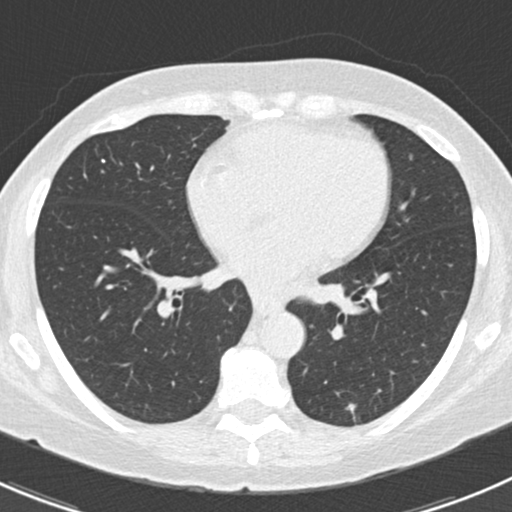
Chest CT (low-dose screening protocol), one axial image. Second screening round (one year after baseline). Lung window (W 1500 / L -600 HU). Slice 86 of 166 in the series. 512 × 512 image matrix. Female, age 64 years at enrolment.
Expert-annotated lung lesion, bounding box [x1, y1, x2, y2] px = [328, 392, 379, 435]. Reader record for this screening exam (exam-level; its link to the box is not recorded): non-calcified nodule or mass ≥4 mm, left lower lobe, 8 × 3 mm, poorly defined margins, soft tissue attenuation, pre-existing on the prior screen: yes; interval growth: no. Later outcome: lung cancer diagnosed 101 days after this screen — adenocarcinoma, NOS, left lower lobe, poorly differentiated (G3), stage IA (AJCC 6th edition), 8 mm at pathology.